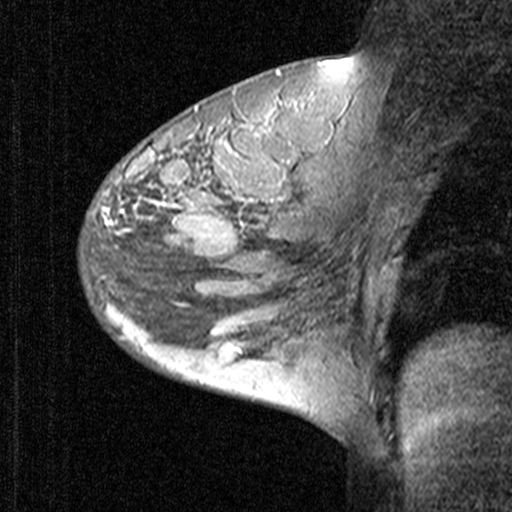
Breast MRI (dynamic contrast-enhanced), one sagittal slice. Slice 29 of 44 in the series (ordered by position). Dynamic contrast-enhanced study with each time point stored as its own series, time point 2 of 3 at this slice position (early post-contrast, ordered by acquisition time). 1.5 T. TE 4.5 ms, TR 11 ms. 3 mm slice thickness. 512 × 512 image matrix, field of view 200 × 200 mm. Patient: female, 27 years. From the clinical record (not read from this slice): setting: breast cancer imaged before/during neoadjuvant chemotherapy; receptor status: HR-positive, HER2-negative.
Annotated regions visible in this slice (semi-automatic segmentation, software-assisted and operator-edited):
- analysis volume of interest (the breast-tissue region the enhancement analysis was run in; not a lesion): bounding box (x1, y1, x2, y2) in pixels: (79, 146, 165, 239)
- tumour enhancement mask (voxels above the 90 % enhancement threshold inside the analysis volume of interest): (139, 189, 164, 198)